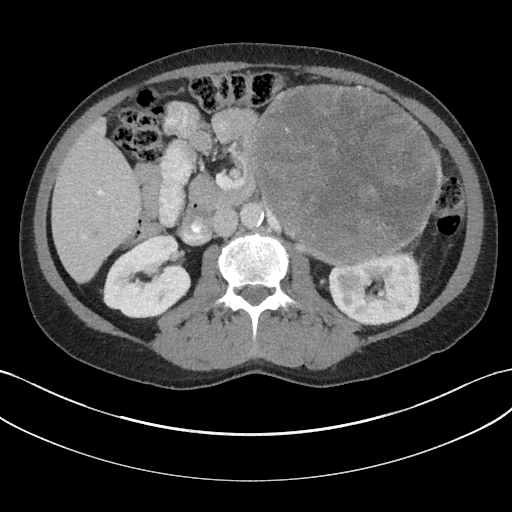
Contrast-enhanced abdominal CT, one axial slice; slice 94 of 147 in the series (ordered by position); reconstruction kernel I31f/3; 100 kVp; intravenous contrast given; soft-tissue window (W 400 / L 40 HU); 3 mm slice thickness; 512 × 512 image matrix, field of view 384 × 384 mm. Male patient, age 58 years. From the clinical record (not read from this slice): diagnosis: adrenocortical carcinoma; tumour side: left adrenal; tumour size at pathology: 22 cm; Ki-67 index: 26 %; stage (as recorded): 2.
Outlined on this slice (semi-automatically segmented with operator editing):
- mass: bounding box (x1, y1, x2, y2) in pixels: (253, 86, 439, 263)